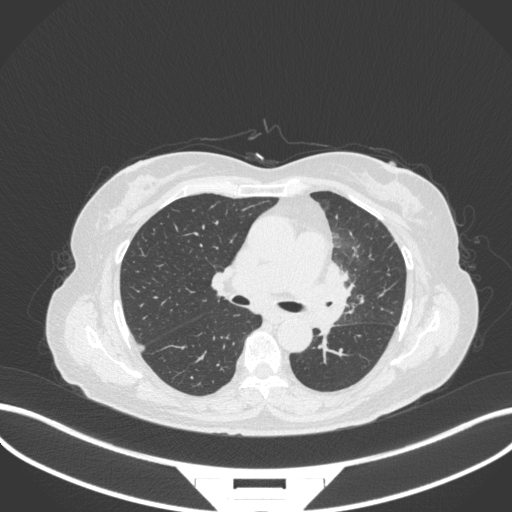
Chest CT, one axial slice; position 198 of 382 along the scan axis; reconstruction kernel B31f; 120 kVp; lung window (W 1500 / L -600 HU); 1 mm slice thickness; 512 × 512 image matrix. Female patient, age 64 years. Case-level facts recorded for this patient, not image findings: clinical TNM (as recorded): T2a N2 M0.
Outlined on this slice (rectangle marked by the reading radiologist):
- lung tumour (recorded histology: adenocarcinoma): box from (x=319, y=255) to (x=356, y=336) px